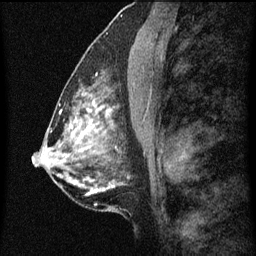
Breast MRI (dynamic contrast-enhanced), one sagittal slice. Position 30 of 60 along the scan axis. Dynamic contrast-enhanced series, image 2 of 7 at this slice position (ordered by acquisition). 1.5 T. TE 4.2 ms, TR 8 ms. 2 mm slice thickness. 256 × 256 image matrix, field of view 180 × 180 mm. Patient: female, 51 years.
Structures marked on this image (semi-automatically segmented with operator editing):
- analysis volume of interest (the breast-tissue region the enhancement analysis was run in; not a lesion): bounding box (x1, y1, x2, y2) in pixels: (86, 48, 114, 101)
- tumour enhancement mask (voxels above the 70 % enhancement threshold inside the analysis volume of interest): (86, 94, 97, 101)